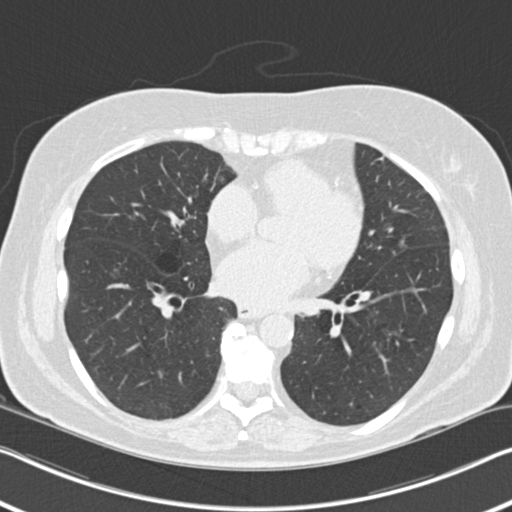
Axial slice from a low-dose chest CT screening exam; second annual screen; lung window (W 1500 / L -600 HU); standard (soft-tissue) reconstruction kernel (B30f). Female participant, aged 60 years at enrolment.
Expert-annotated lung lesion, bounding box [x1, y1, x2, y2] px = [377, 231, 408, 264]. The screening reader recorded 6 non-calcified nodules or masses ≥4 mm on this exam (right upper lobe, right middle lobe, right lower lobe, right lower lobe, left lower lobe, lingula); which of them this box marks is not recorded. Official screen result: positive, change unspecified: nodule(s) >= 4 mm or enlarging nodule(s), mass(es), or other non-specific abnormalities suspicious for lung cancer. Later outcome: lung cancer diagnosed 495 days after this screen — non-small cell carcinoma, left upper lobe, poorly differentiated (G3), stage IB (AJCC 6th edition), 7 mm at pathology.